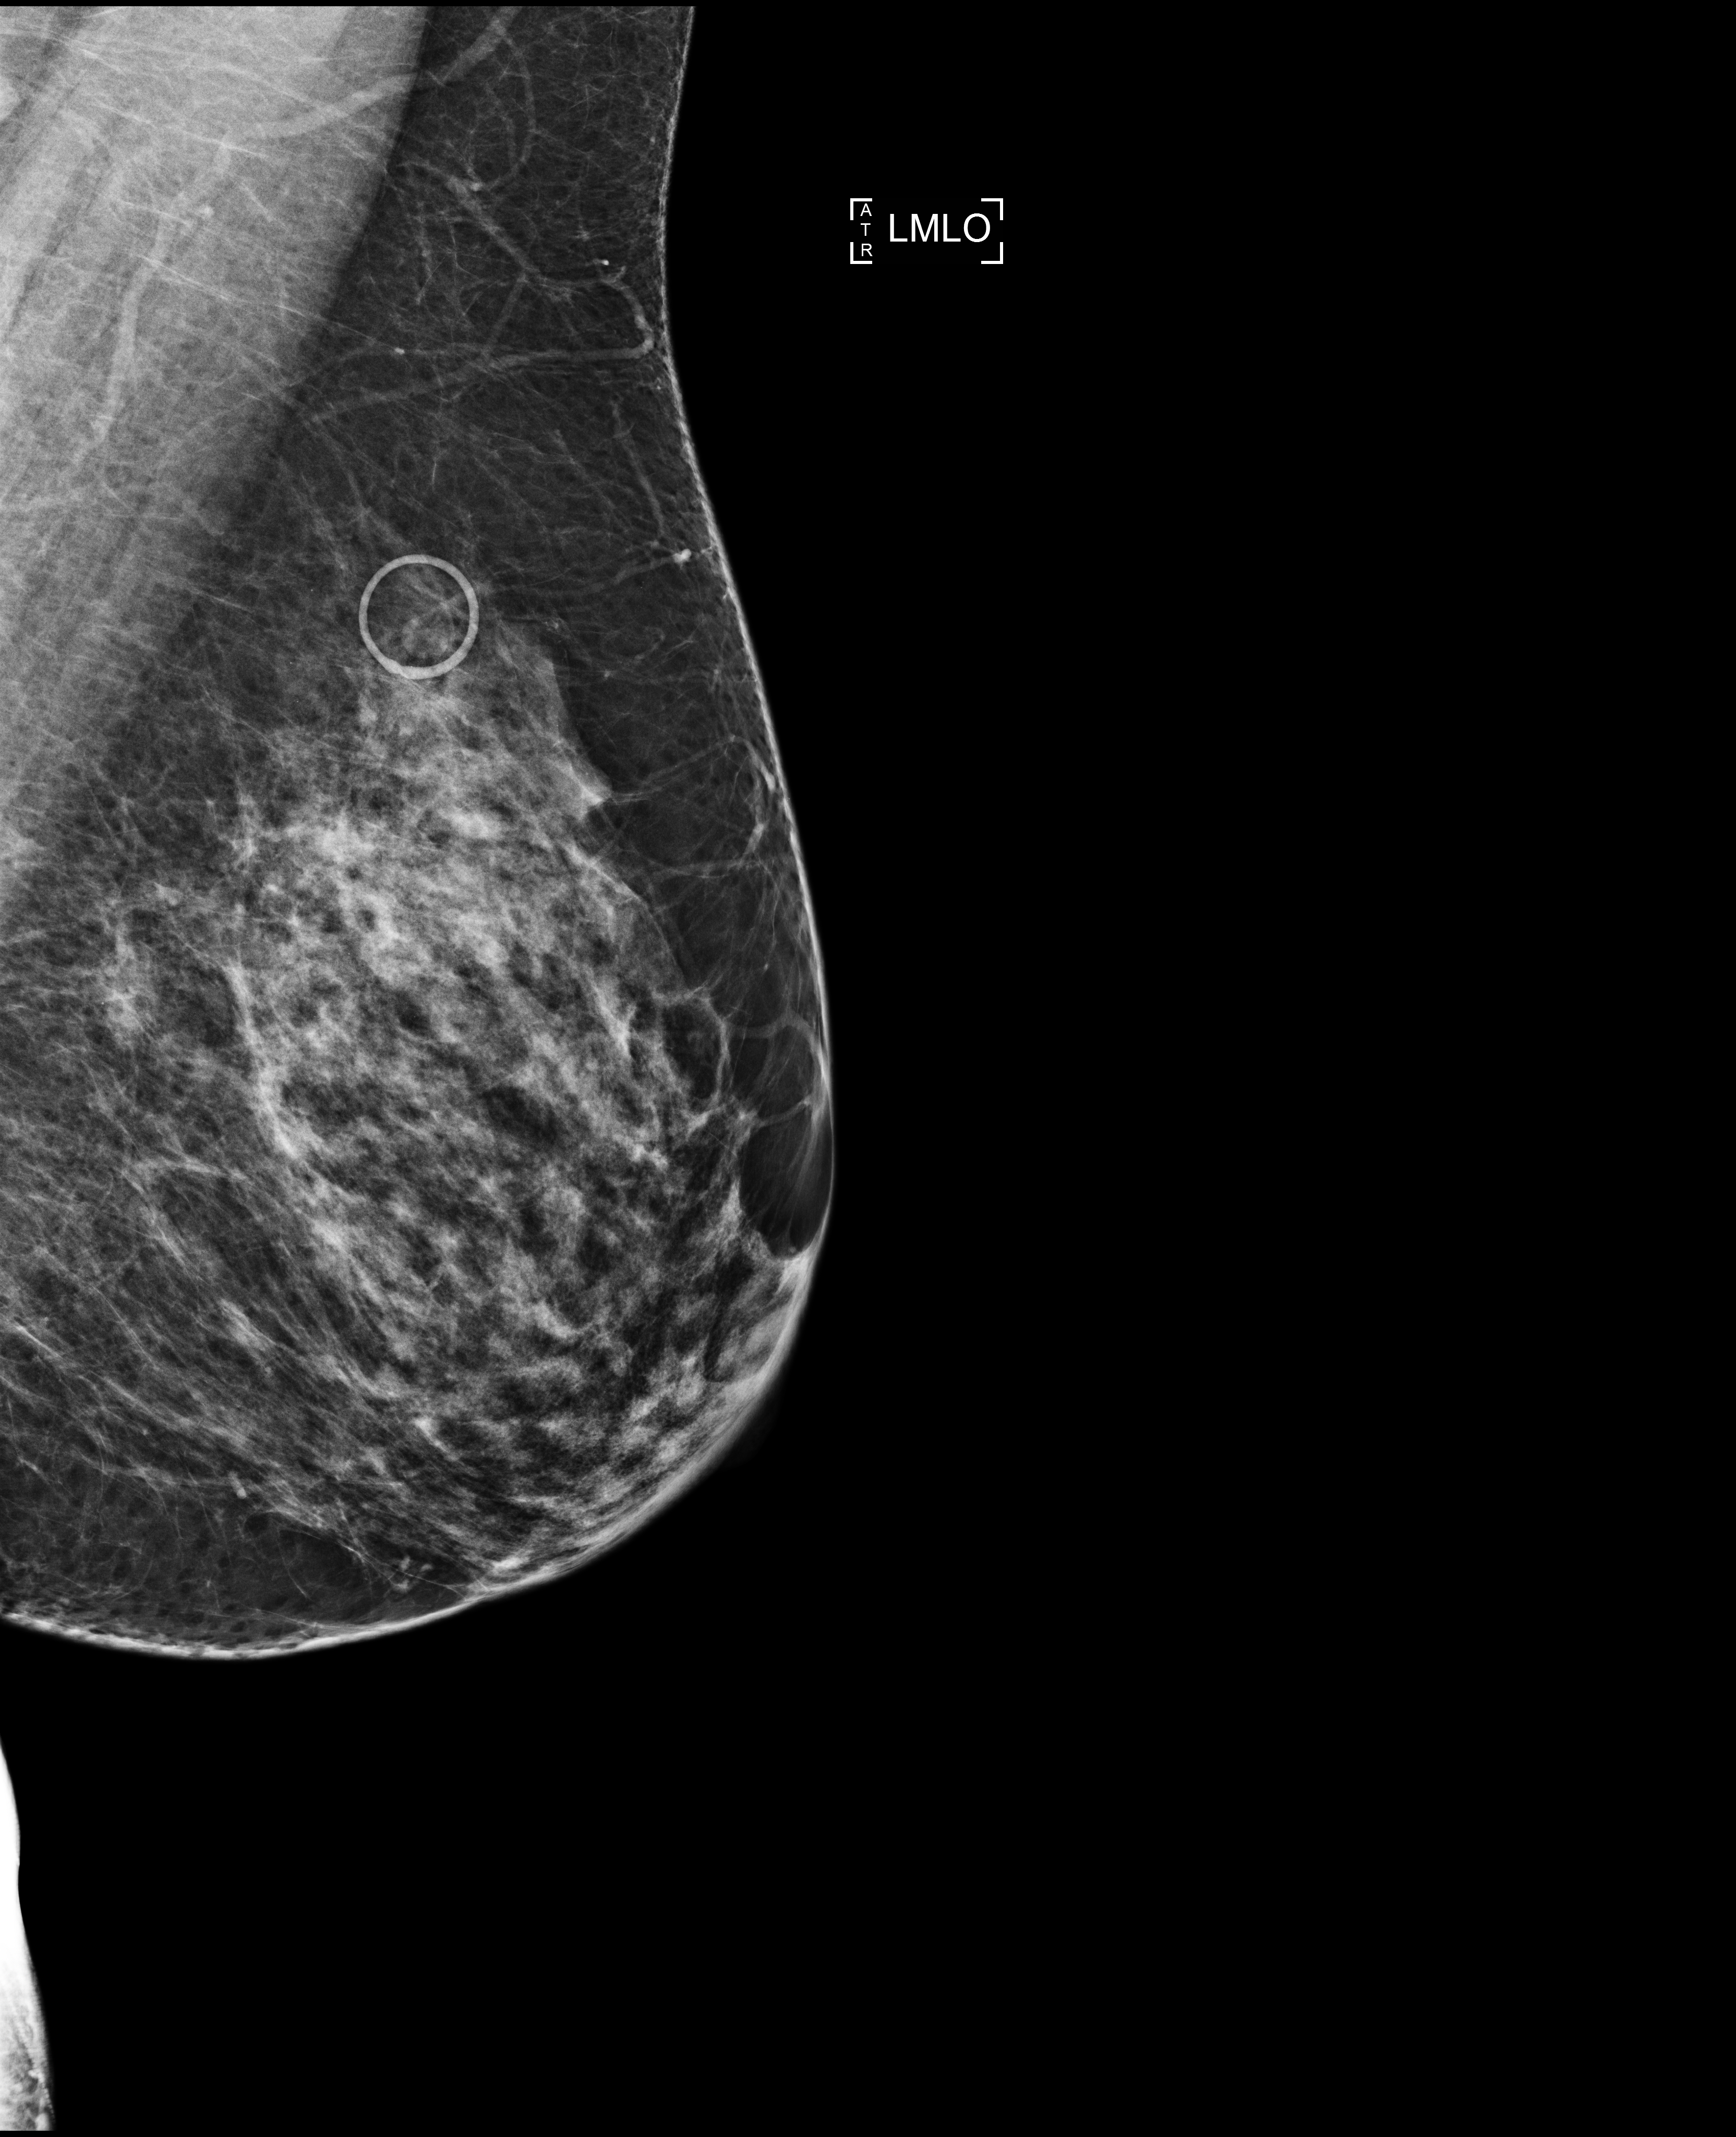
Screening examination; compressed breast thickness 74 mm; system: Selenia Dimensions. Female patient, age 53 years.
Image type: full-field digital mammogram. Breast: left. Projection: medio-lateral oblique projection.